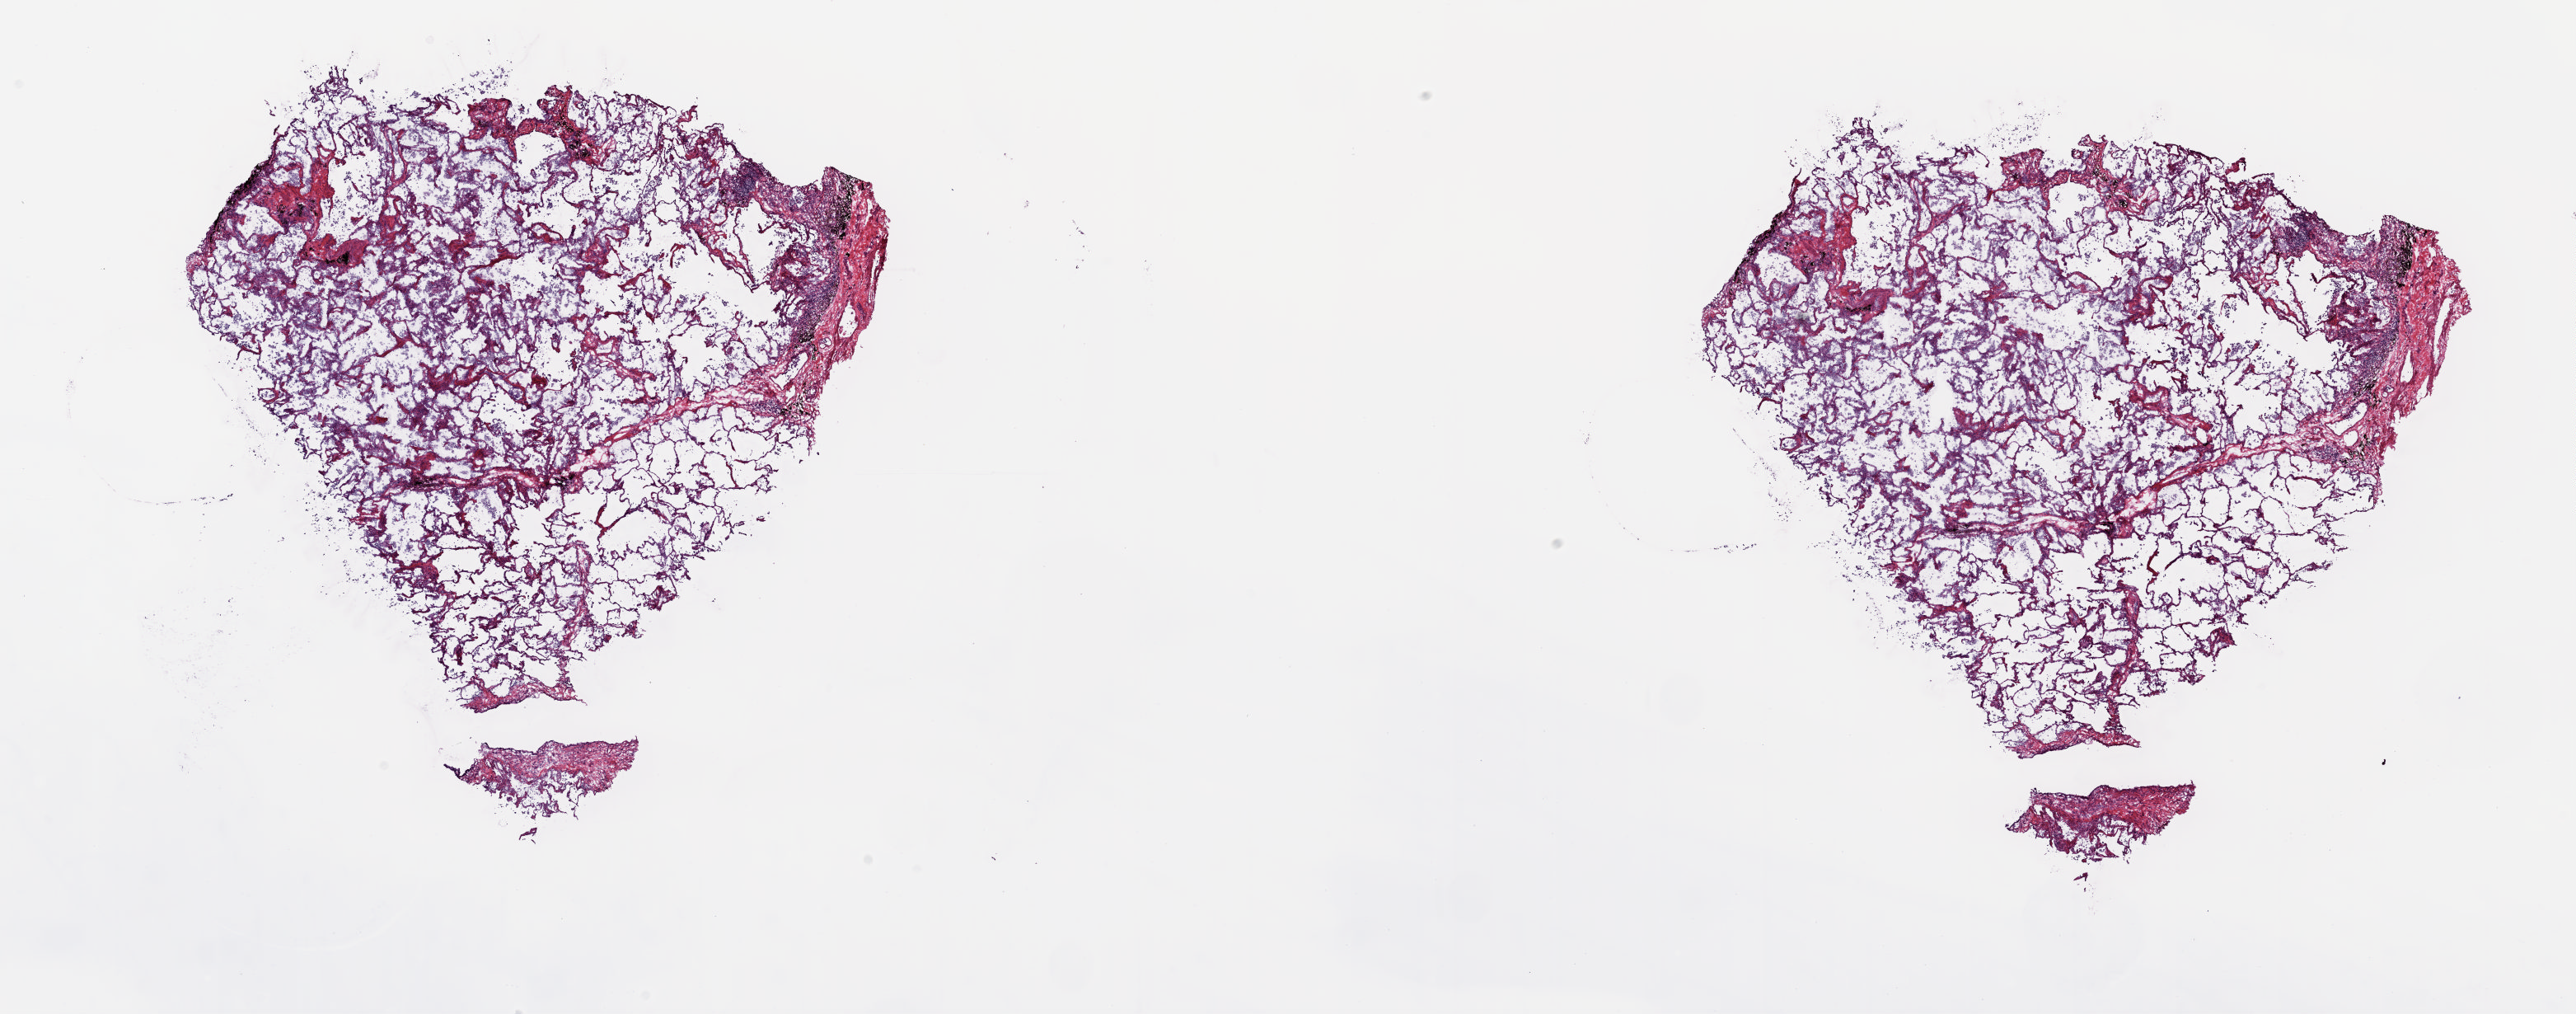
Digitized H&E-stained tissue section (whole slide) — a low-resolution overview of the entire scanned area, about 24.8 x 9.8 mm (acquisition: 20x scan); frozen section; lung, solid tissue normal (non-tumour tissue) sample. Female patient; age at initial diagnosis 57 years. Composition of this section per pathologist review: tumour cells 0%, tumour nuclei 0%, normal cells 100%, stromal cells 0%, necrosis 0%. Inflammatory infiltration, as recorded: lymphocyte infiltration 0%, monocyte infiltration 0%, neutrophil infiltration 0%.
- this section: solid tissue normal (non-tumour) sample from the same patient
- patient diagnosis: Squamous cell carcinoma, NOS (upper lobe, lung)